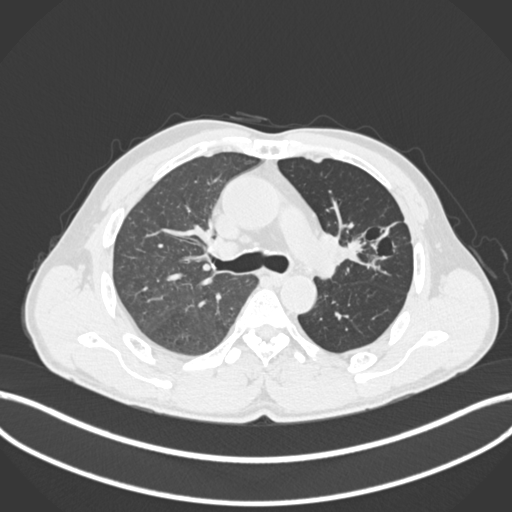
Chest CT, one axial slice. Slice 124 of 255 in the series (ordered by position). Reconstruction kernel B30f. Lung window (W 1500 / L -600 HU). 1 mm slice thickness. 512 × 512 image matrix, field of view 400 × 400 mm. Patient: male, 57 years. From the clinical record (not read from this slice): clinical TNM (as recorded): T2b N0 M0.
Structures marked on this image (bounding box drawn by a radiologist):
- lung tumour (recorded histology: squamous cell carcinoma): bounding box [x1, y1, x2, y2] px = [319, 225, 376, 269]